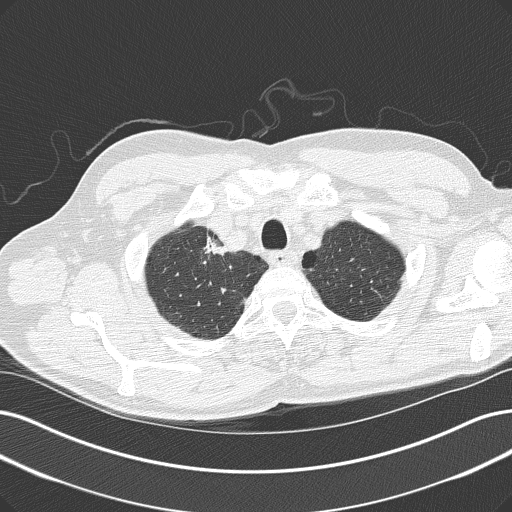
Axial slice from a low-dose chest CT screening exam. Baseline screening round. Lung window (W 1500 / L -600 HU). 2 mm slice thickness. 120 kVp. Slice 23 of 152 in the series. Male, age 61 years at enrolment. Current smoker at enrolment.
Lesion marked by an expert reader, bounding box (x1, y1, x2, y2) in pixels: (193, 227, 246, 272). The screening reader recorded 2 non-calcified nodules or masses ≥4 mm on this exam; which of them this box marks is not recorded.